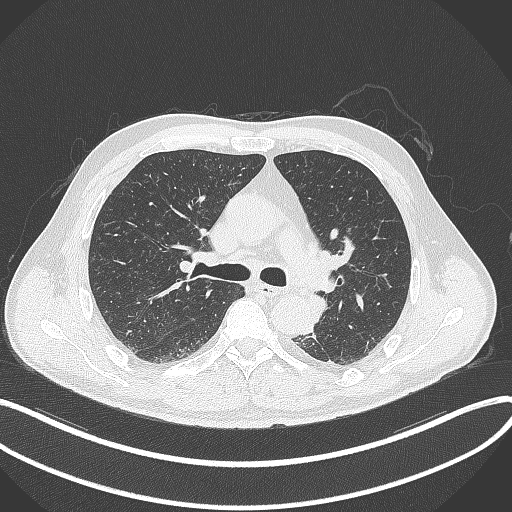
Chest CT, one axial slice. Reconstruction kernel B70f. Lung window (W 1500 / L -600 HU). 1 mm slice thickness. 512 × 512 image matrix, field of view 400 × 400 mm. Patient: male, 59 years. From the clinical record (not read from this slice): clinical TNM (as recorded): T2a N2 M0.
Annotated regions visible in this slice (bounding box drawn by a radiologist):
- lung tumour (recorded histology: squamous cell carcinoma): bounding box [x1, y1, x2, y2] px = [305, 290, 329, 326]